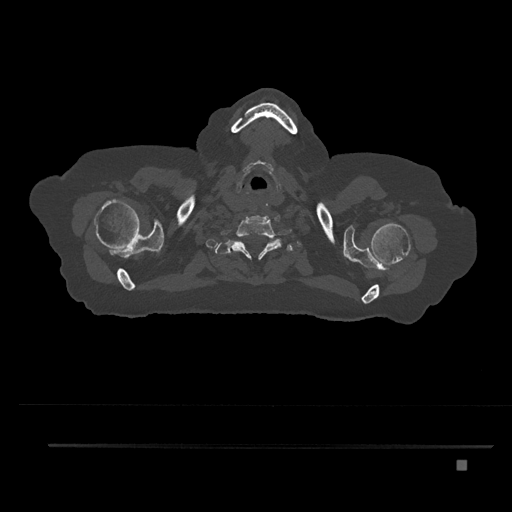
CT including the spine, one axial slice. Slice 717 of 797 in the series (ordered by position). 120 kVp. Bone window (W 1800 / L 400 HU). 0.5 mm slice thickness. 512 × 512 image matrix, field of view 437 × 437 mm. Female patient, age 76 years. From the clinical record (not read from this slice): primary cancer: lung.
Structures marked on this image (semi-automatic segmentation, software-assisted and operator-edited):
- T1 vertebra: bounding box (x1, y1, x2, y2) in pixels: (221, 242, 263, 258)